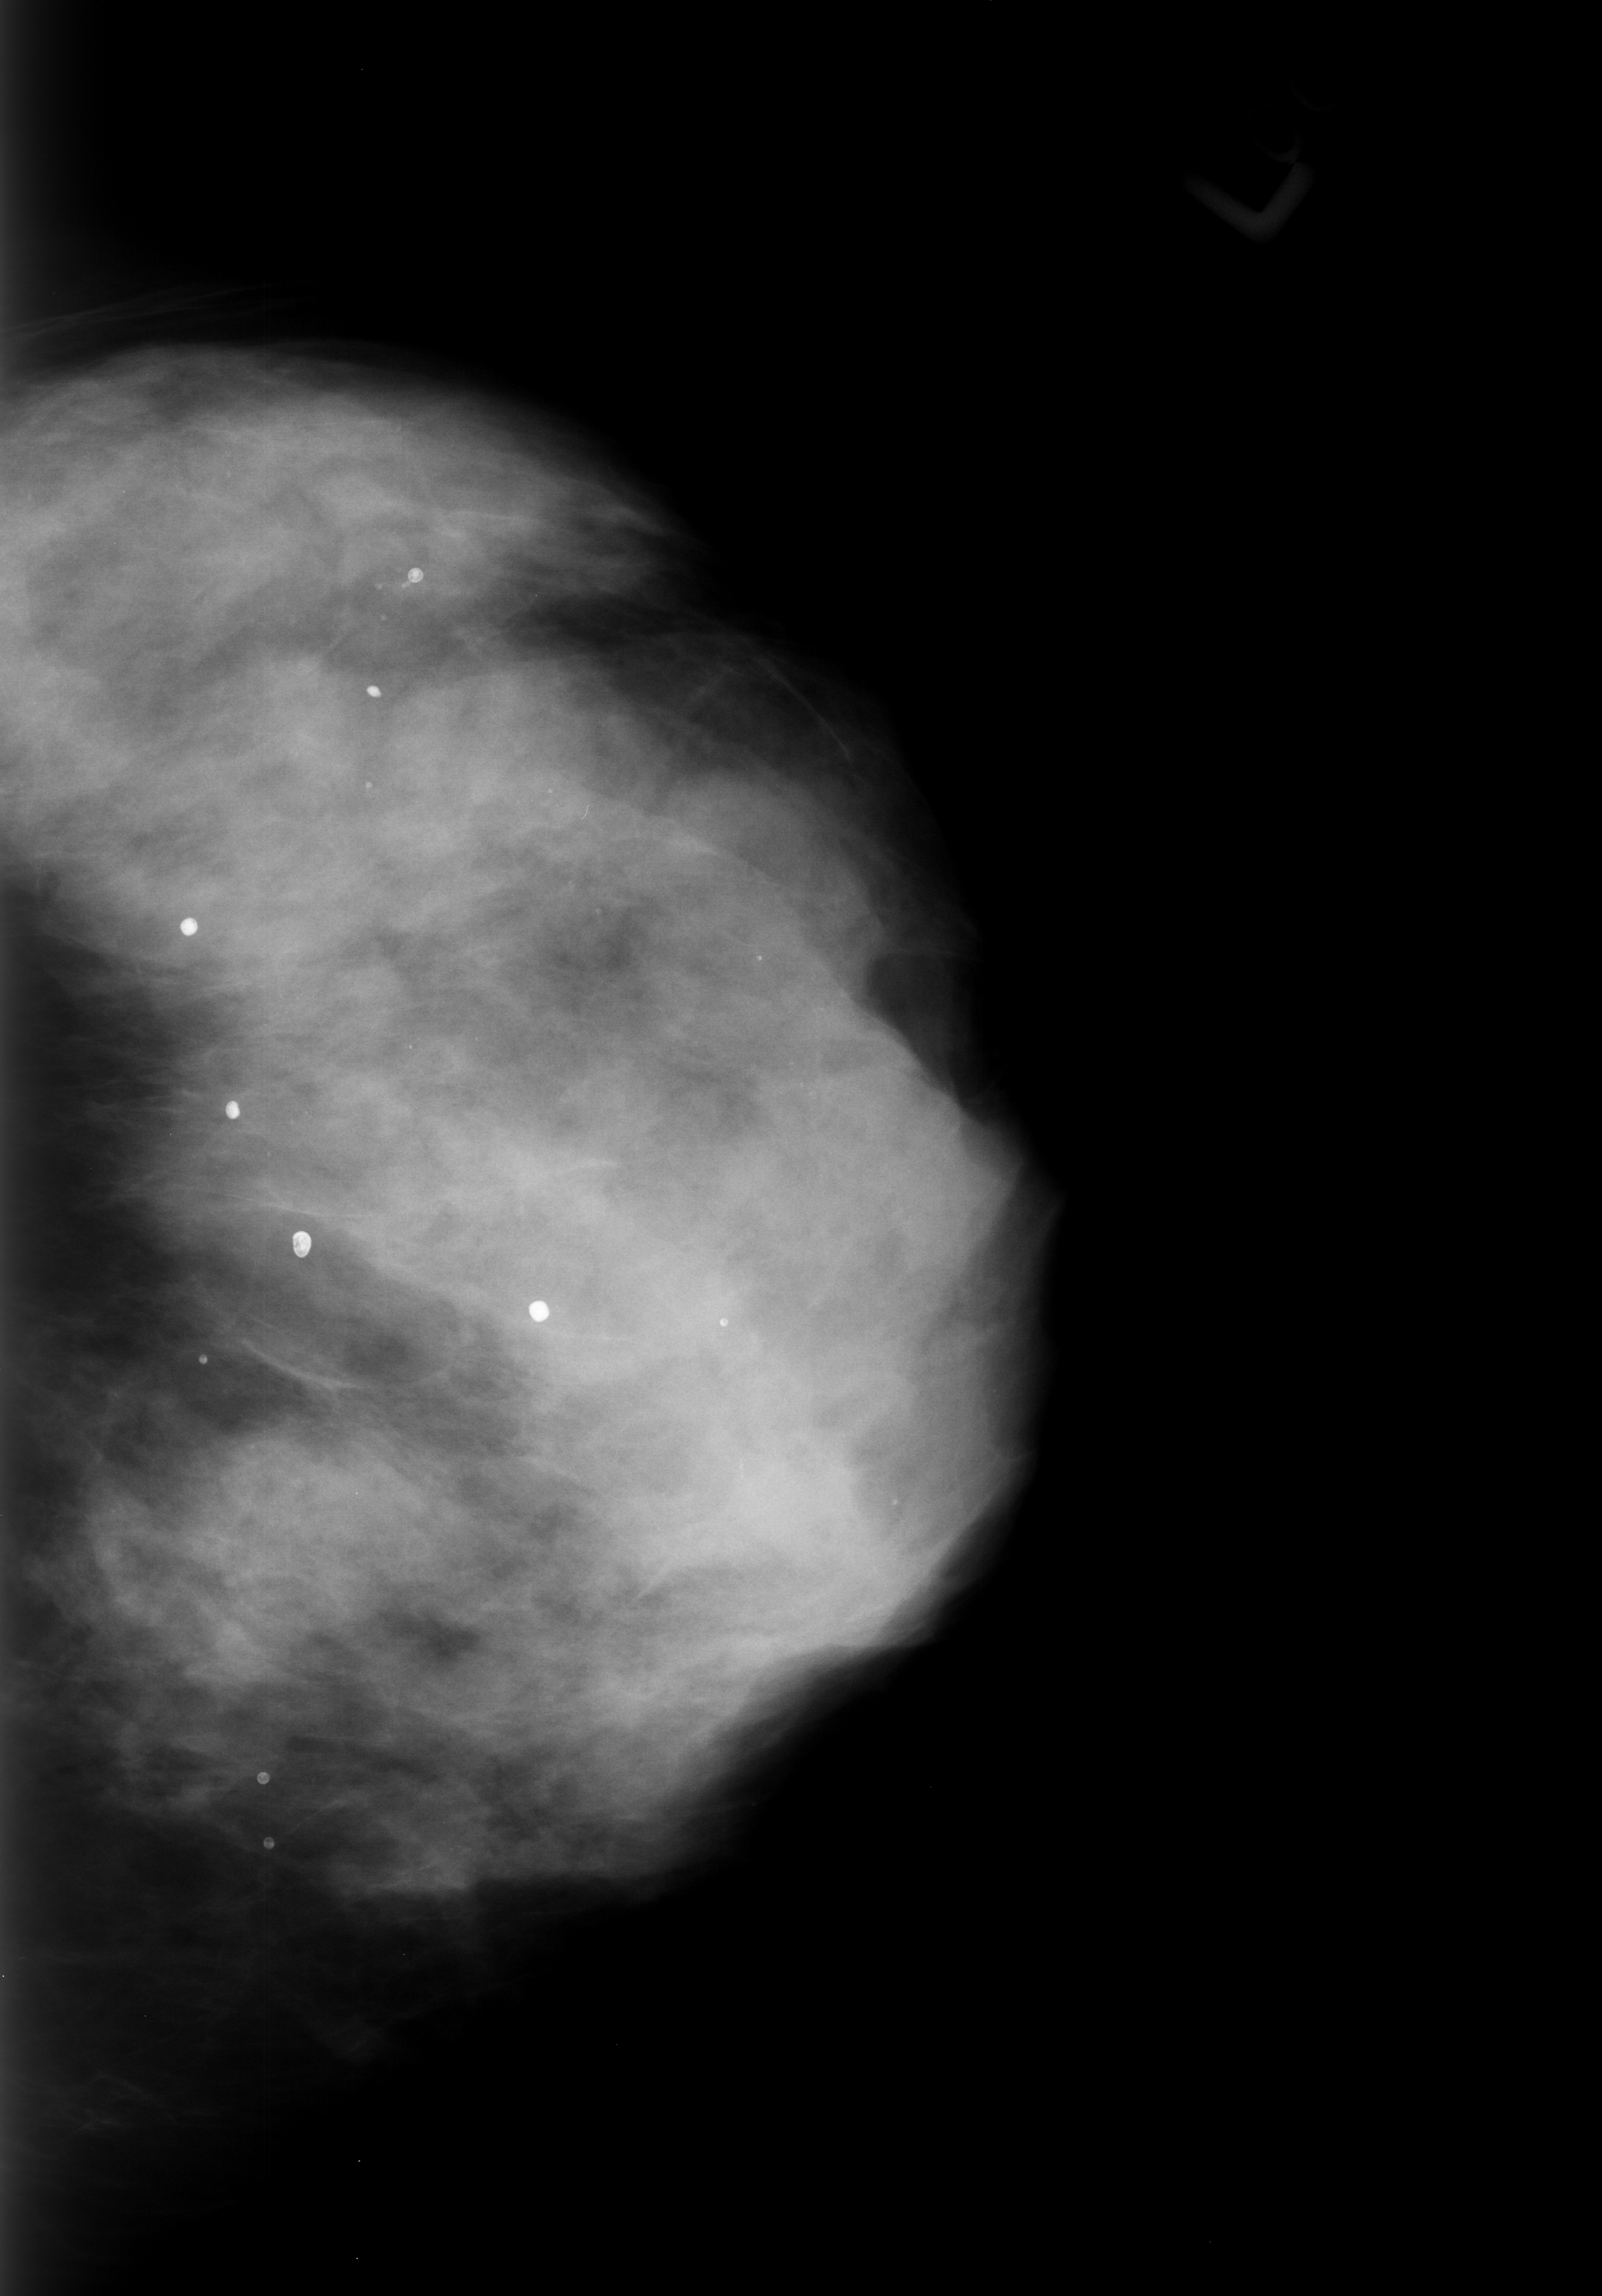
Digitized screen-film mammogram; left breast; CC view; BI-RADS breast density category 4 (scale 1–4); 1602 × 2296 image matrix.
Marked abnormalities (boxes around the expert regions of interest):
- Finding 1 of 6: calcifications, morphology round and regular / lucent center / punctate, distribution diffusely scattered; BI-RADS assessment category 2; benign; no additional work-up was recommended (outcome (as recorded, no biopsy): benign without callback): bounding box [x1, y1, x2, y2] px = [163, 896, 229, 949]
- Finding 2 of 6: calcifications, morphology round and regular / lucent center / punctate, distribution diffusely scattered; BI-RADS assessment category 2; subtlety rating 5 on a 1 (subtle) to 5 (obvious) scale; benign; no additional work-up was recommended (outcome (as recorded, no biopsy): benign without callback): [206, 1068, 272, 1130]
- Finding 3 of 6: calcifications, morphology round and regular / lucent center / punctate, distribution diffusely scattered; BI-RADS assessment category 2; benign; no additional work-up was recommended (outcome (as recorded, no biopsy): benign without callback): [275, 1210, 333, 1276]
- Finding 4 of 6: calcifications, morphology round and regular / lucent center / punctate, distribution diffusely scattered; BI-RADS assessment category 2; subtlety rating 5 on a 1 (subtle) to 5 (obvious) scale; outcome (as recorded, no biopsy): benign without callback (not worked up further): [344, 672, 406, 720]
- Finding 5 of 6: calcifications, morphology round and regular / lucent center / punctate, distribution diffusely scattered; BI-RADS assessment category 2; benign; no additional work-up was recommended (outcome (as recorded, no biopsy): benign without callback): [391, 551, 445, 604]
- Finding 6 of 6: calcifications, morphology round and regular / lucent center / punctate, distribution diffusely scattered; BI-RADS assessment category 2; outcome (as recorded, no biopsy): benign without callback (not worked up further): [512, 1283, 565, 1349]